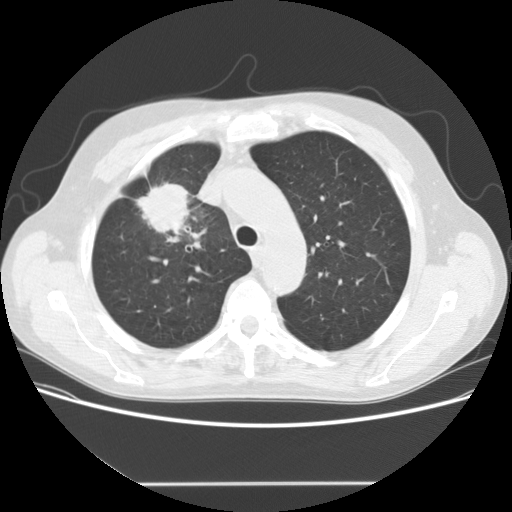
Chest CT (low-dose screening protocol), one axial image; baseline annual screen; lung window (W 1500 / L -600 HU); 2.5 mm slice thickness; slice 38 of 153 in the series; 512 × 512 image matrix, field of view 360 × 360 mm. Male, age 56 years at enrolment. Current smoker at enrolment.
Expert-annotated lung lesion, box from (x=128, y=172) to (x=214, y=246) px. The screening reader recorded 2 non-calcified nodules or masses ≥4 mm on this exam (right upper lobe, right middle lobe); which of them this box marks is not recorded. Later outcome: lung cancer diagnosed 120 days after this screen — adenocarcinoma, NOS, right upper lobe, stage IIIA (AJCC 6th edition), 34 mm at pathology.